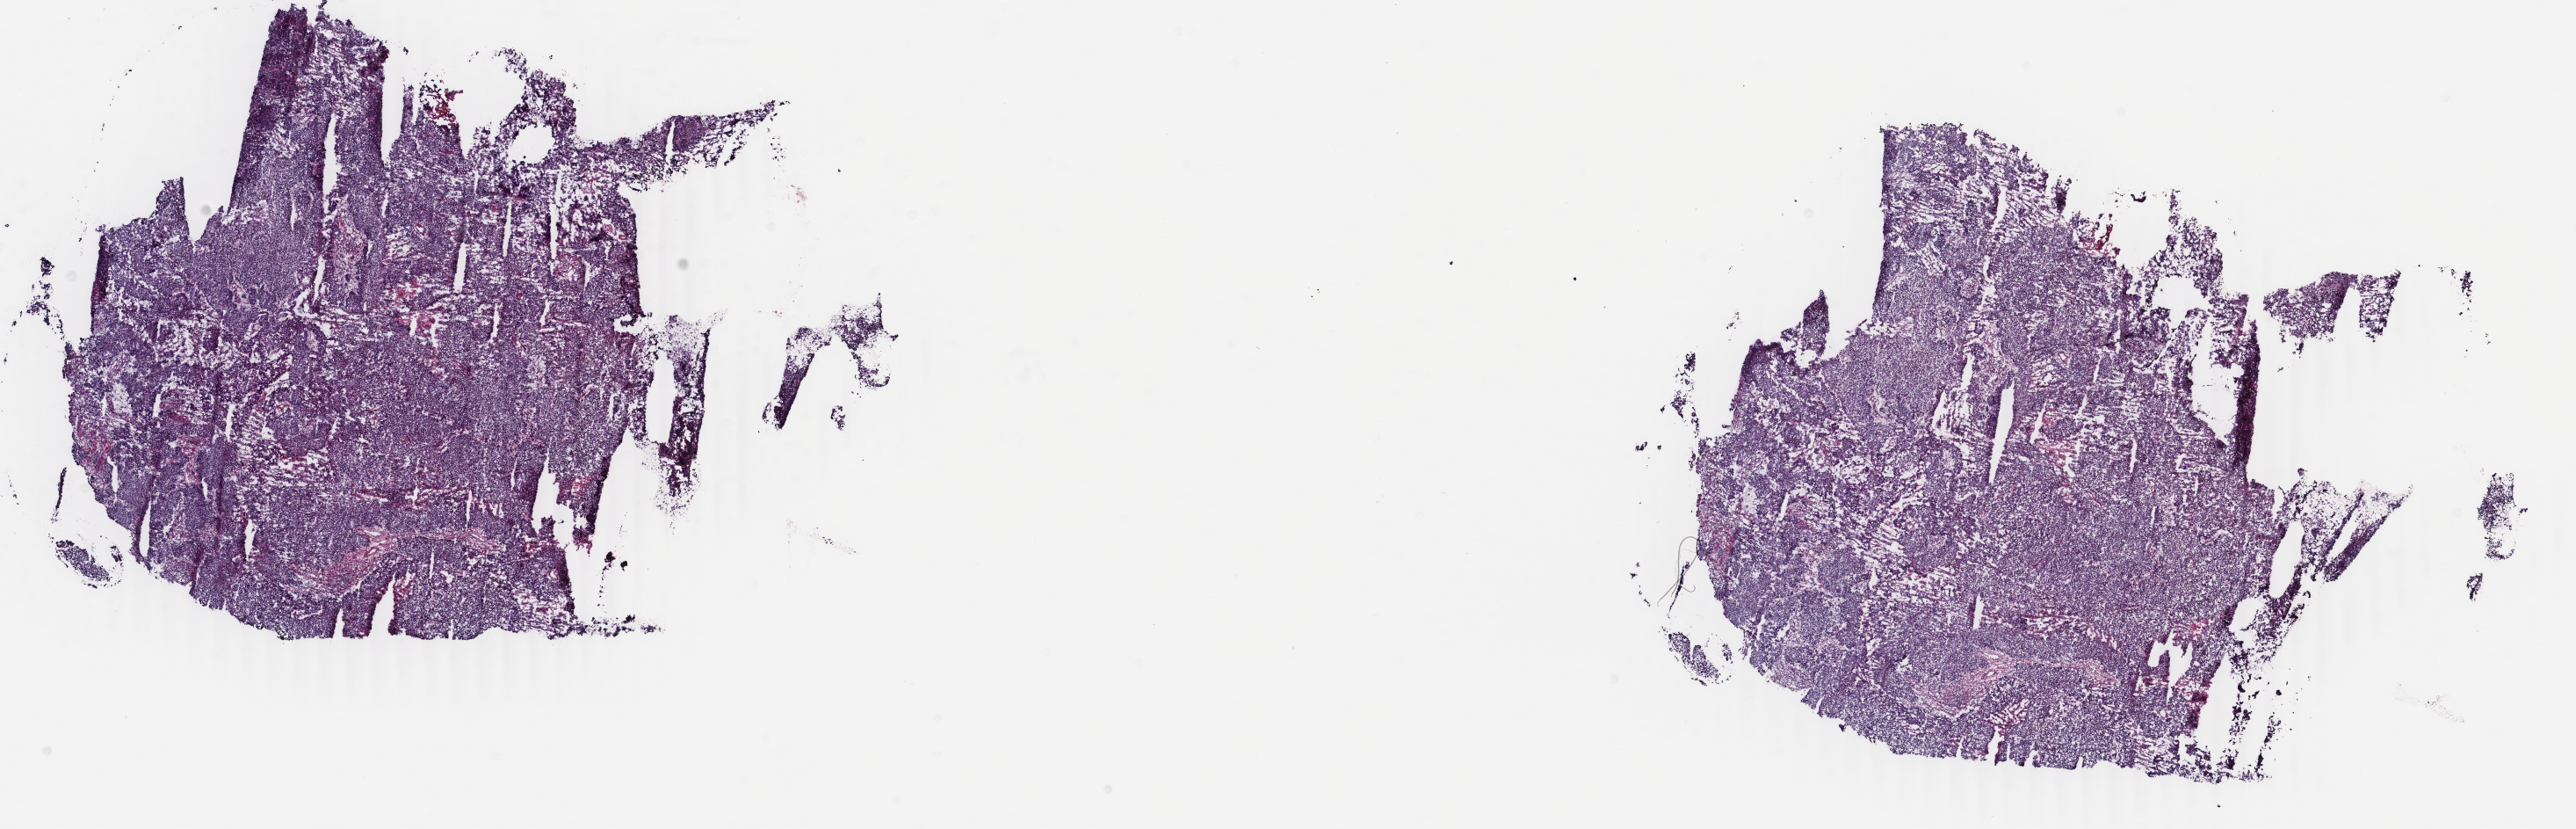
Digitized Hematoxylin and eosin (H&E) stained tissue section (whole slide), a low-resolution overview of the entire scanned area, about 23.3 x 7.5 mm. Frozen section from the top of the tissue portion. Sample: primary tumour, uterus. Female, age 53 years at initial diagnosis. Histologic grade: G3 (poorly differentiated). Composition of this section per pathologist review: tumour cells 95%, tumour nuclei 95%, normal cells 0%, stromal cells 3%, necrosis 2%. Infiltration values recorded for this section: lymphocyte infiltration 4%, monocyte infiltration 0%, neutrophil infiltration 1%.
Diagnosis: Endometrioid adenocarcinoma, NOS (endometrium). Lymph nodes positive (case pathology): 0 of 4 examined. FIGO stage: IB.